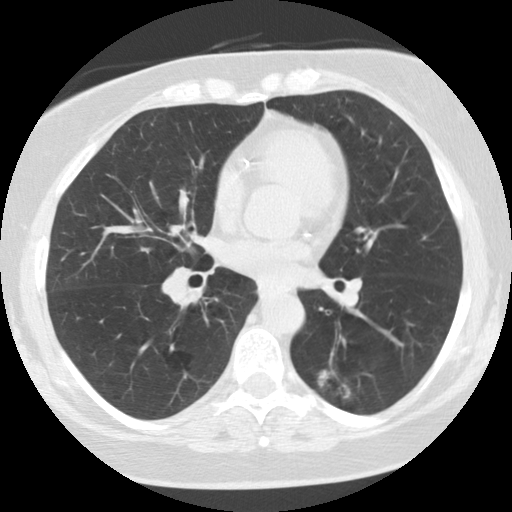
Chest CT (low-dose screening protocol), one axial image, baseline annual screen, lung window (W 1500 / L -600 HU), standard (soft-tissue) reconstruction kernel (STANDARD), slice 63 of 115 in the series. Female, age 59 years at enrolment.
• Lesion marked by an expert reader, bounding box [x1, y1, x2, y2] px = [295, 352, 366, 418].
• The screening reader recorded 5 non-calcified nodules or masses ≥4 mm on this exam (right upper lobe, right lower lobe, left lower lobe, right lower lobe, left lower lobe); which of them this box marks is not recorded.
• Participant outcome: lung cancer diagnosed 707 days after this screen — adenocarcinoma, NOS, left lower lobe, poorly differentiated (G3), stage IA (AJCC 6th edition), 15 mm at pathology.